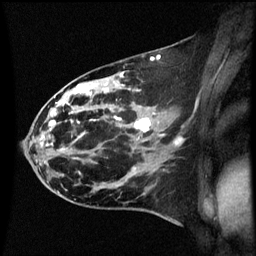
Breast MRI (dynamic contrast-enhanced), one sagittal slice. Position 31 of 60 along the scan axis. Dynamic contrast-enhanced series, image 2 of 3 at this slice position (ordered by acquisition). 1.5 T. TE 4.2 ms, TR 8.9 ms. 2 mm slice thickness. 256 × 256 image matrix, field of view 200 × 200 mm. Female patient, age 44 years. Case-level facts recorded for this patient, not image findings: setting: breast cancer imaged before/during neoadjuvant chemotherapy; receptor status: HR-positive, HER2-negative.
Outlined on this slice (semi-automatically segmented with operator editing):
- analysis volume of interest (the breast-tissue region the enhancement analysis was run in; not a lesion): box from (x=43, y=78) to (x=153, y=189) px
- tumour enhancement mask (voxels above the 70 % enhancement threshold inside the analysis volume of interest): (x=49, y=80)–(x=151, y=171)